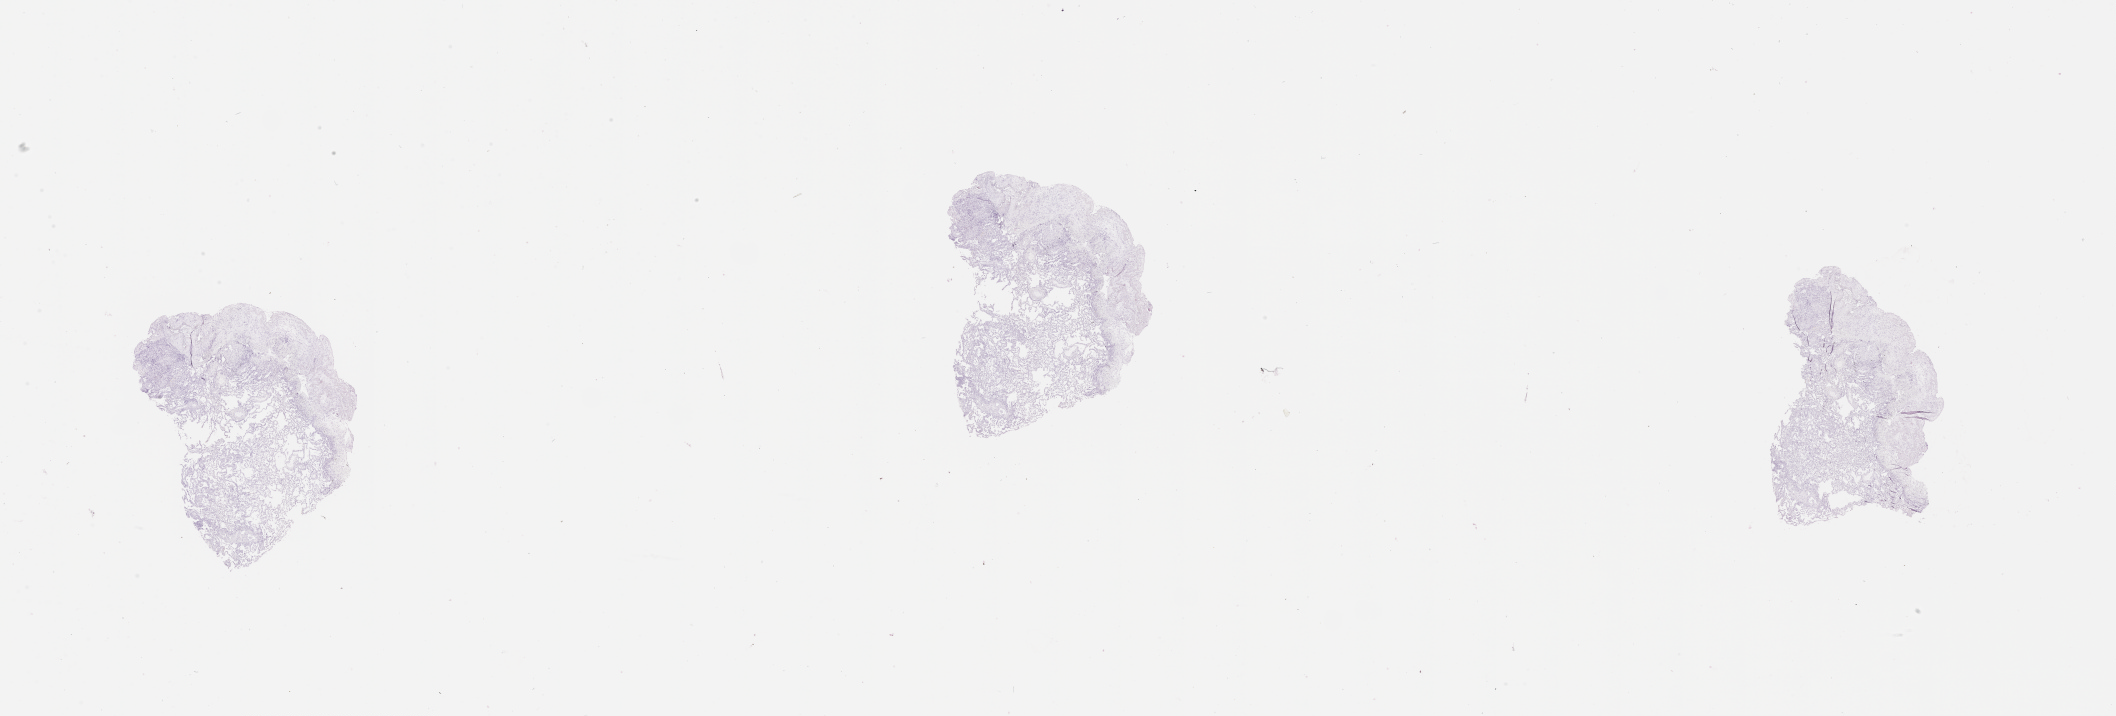
Digitized H&E tissue section (whole slide), a low-resolution overview of the entire scanned area, about 34.1 x 11.5 mm (acquisition: 20x scan); lung, normal (non-tumour) tissue. Male, 66 y/o.
This section: normal (non-tumour) tissue from the same patient. Patient diagnosis (cohort enrolment): squamous cell carcinoma (lung).